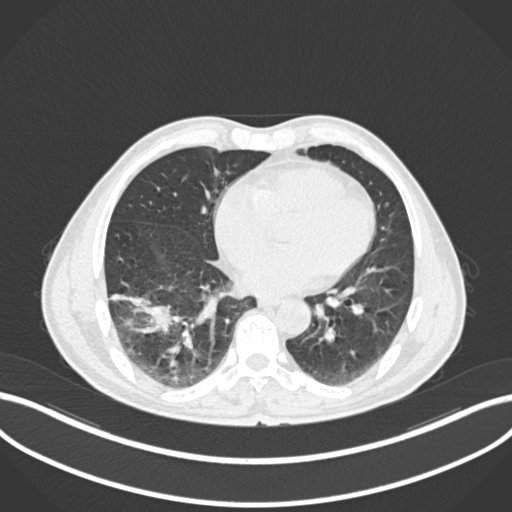
Chest CT, one axial slice. Position 64 of 208 along the scan axis. 120 kVp. Lung window (W 1500 / L -600 HU). 1 mm slice thickness. 512 × 512 image matrix. Patient: male, 58 years. Case-level facts recorded for this patient, not image findings: clinical TNM (as recorded): T3 N0 M0; histopathological grade: G2.
Outlined on this slice (bounding box drawn by a radiologist):
- lung tumour (recorded histology: squamous cell carcinoma): bounding box (x1, y1, x2, y2) in pixels: (113, 288, 173, 339)